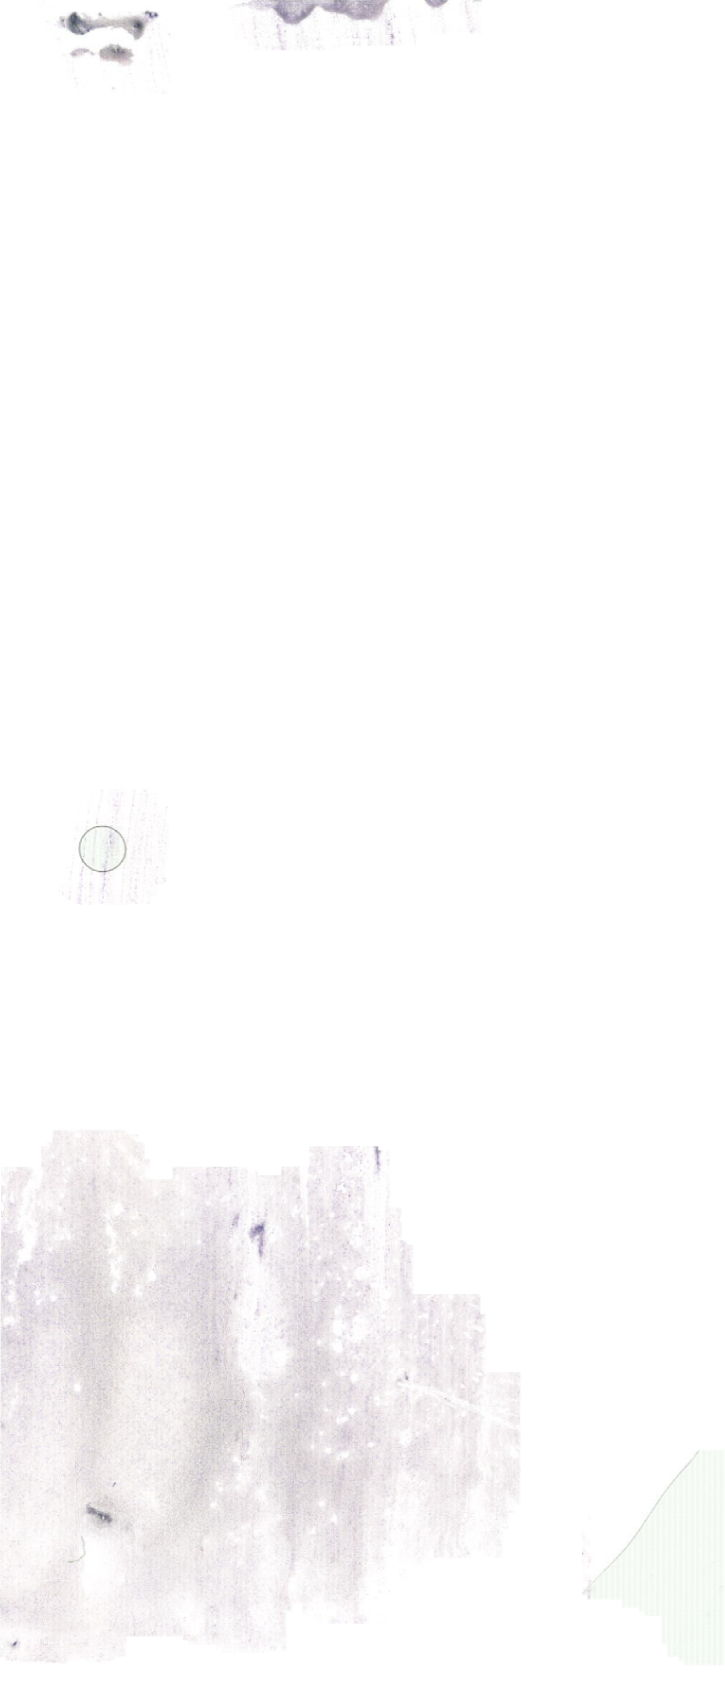
Whole-slide image of a May-Grünwald–Giemsa-stained bone marrow aspirate smear, shown as a low-resolution overview of the whole scanned area (about 20.6 x 47.9 mm). Patient sex: male.